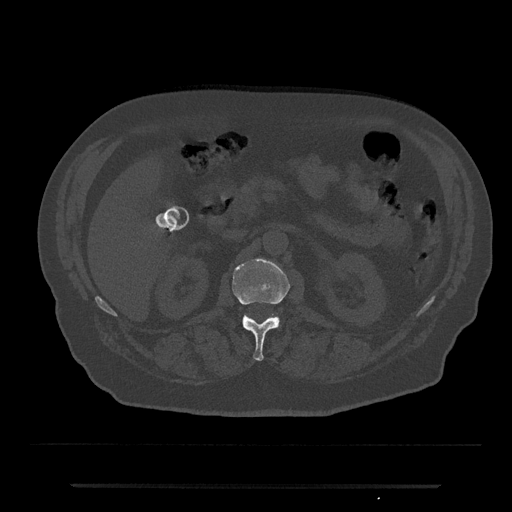
CT including the spine, one axial slice; slice 524 of 797 in the series (ordered by position); 120 kVp; bone window (W 1800 / L 400 HU); 0.5 mm slice thickness; 512 × 512 image matrix, field of view 434 × 434 mm. Patient: male, 80 years. Case-level facts recorded for this patient, not image findings: primary cancer: prostate; vertebrae with lytic lesions (as recorded): L1, T11.
Outlined on this slice (semi-automatic segmentation, software-assisted and operator-edited):
- L1 vertebra: bounding box <232,259,290,361> (left, top, right, bottom; pixels)